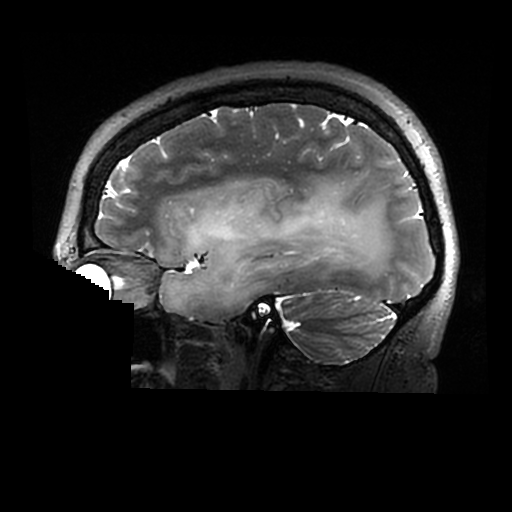
Brain MRI from a brain-tumour surgery series, one sagittal slice; slice 206 of 320 in the series (ordered by position); 0.6 mm slice thickness; 512 × 512 image matrix, field of view 240 × 240 mm. Case-level facts recorded for this patient, not image findings: histopathology: Astrocytoma; WHO grade: 2; IDH mutation: yes.
Annotated regions visible in this slice (manually delineated by an expert):
- tumour: bounding box (x1, y1, x2, y2) in pixels: (161, 180, 390, 312)